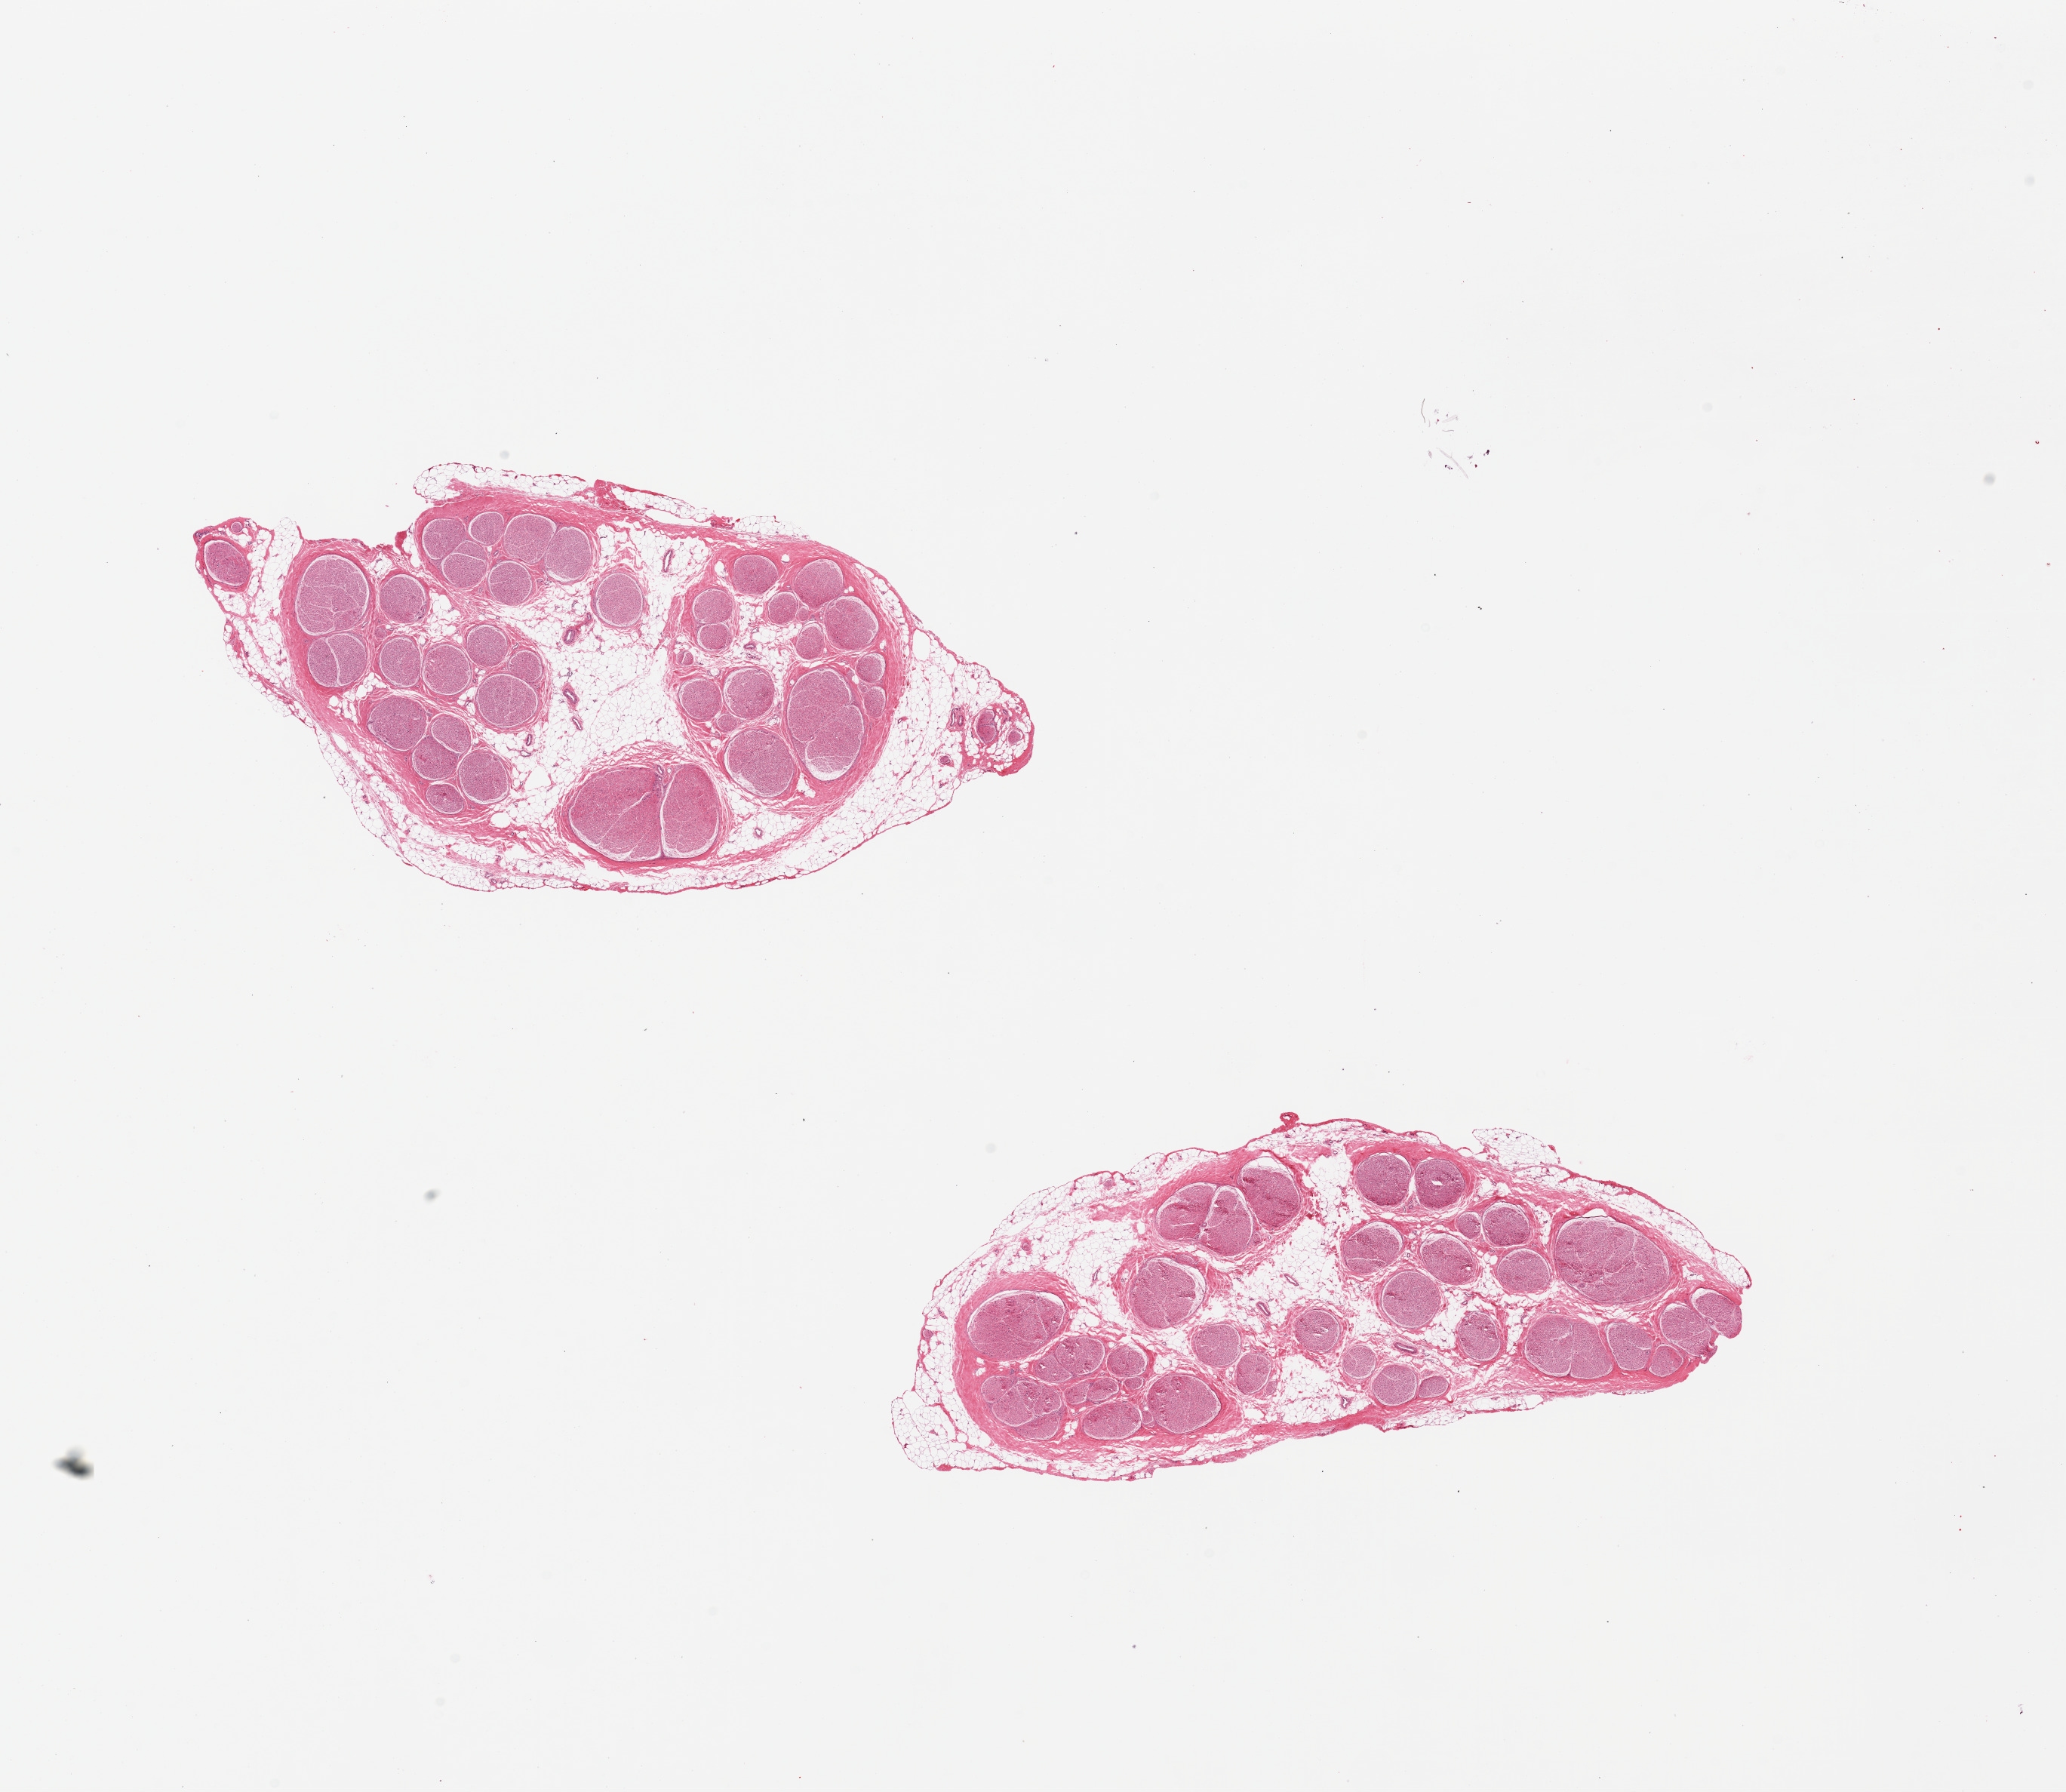
Whole-slide image, haematoxylin and eosin stain — low-resolution overview of the scanned area, about 21.7 x 18.8 mm. PAXgene-fixed paraffin-embedded (PFPE) section. Sampled site (target tissue): tibial nerve. Tissue donor sample. Donor: male.
Review note (as recorded): 2 pieces 40% internal and external fat.